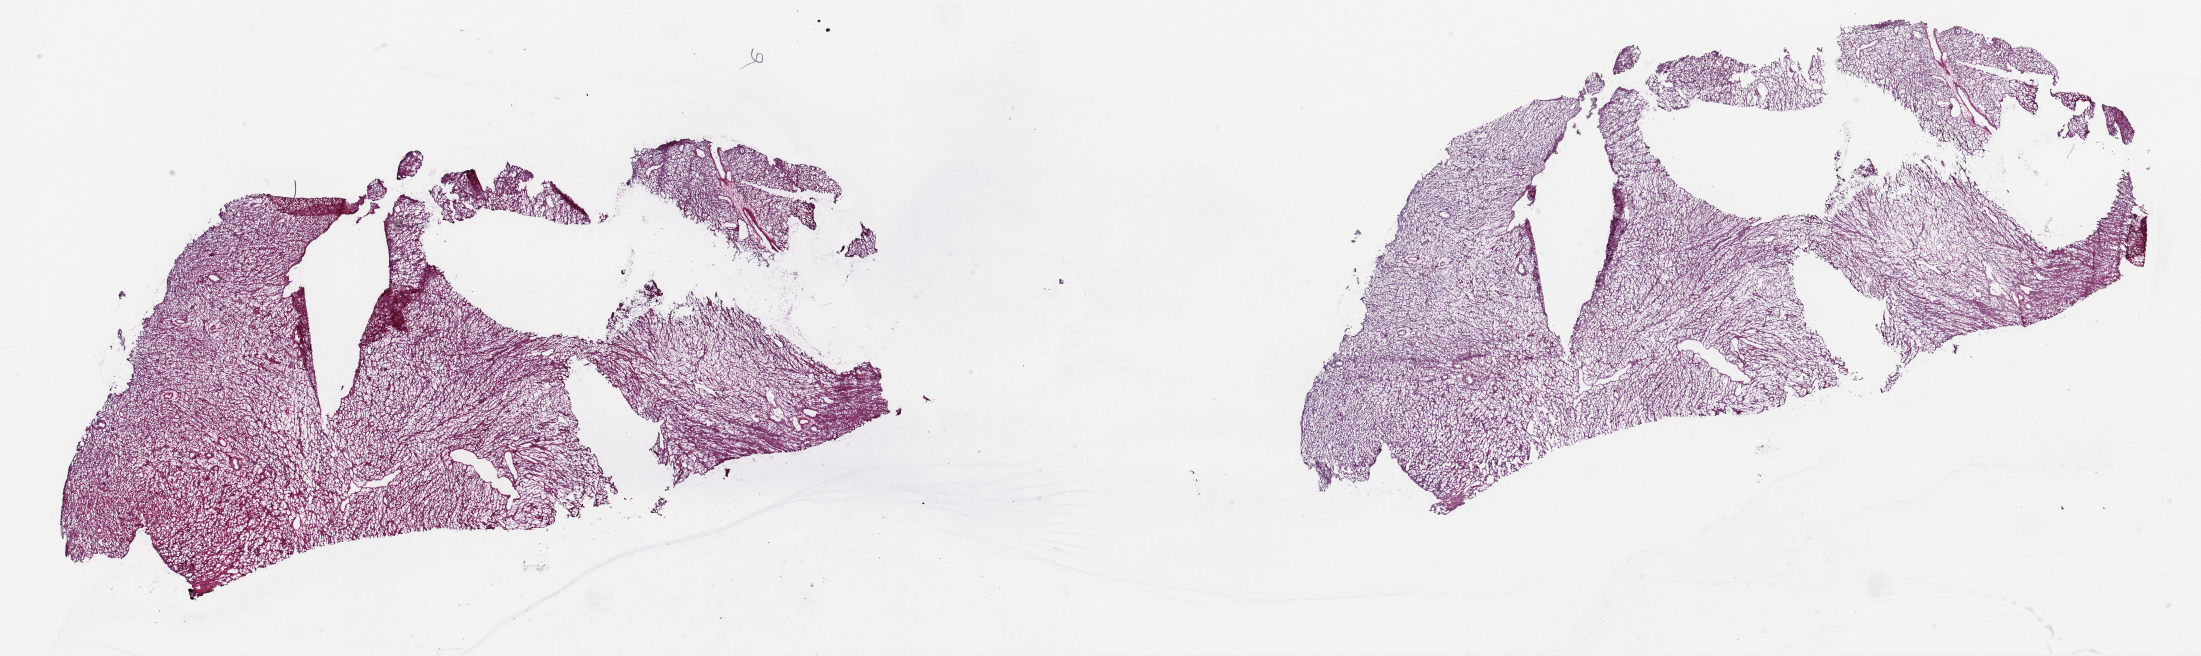
Digitized H&E tissue section (whole slide), low-resolution overview of the scanned area, about 34.8 x 10.4 mm (acquisition: 40x scan). Frozen section. Uterus, primary tumour sample. Female, age 44 years at initial diagnosis. Pathologist review of this section (percent, as recorded): tumour cells 95%, tumour nuclei 95%, normal cells 0%, stromal cells 5%, necrosis 0%. Inflammatory infiltration, as recorded: lymphocyte infiltration 0%, monocyte infiltration 0%, neutrophil infiltration 0%.
Diagnosis: Myxoid leiomyosarcoma.